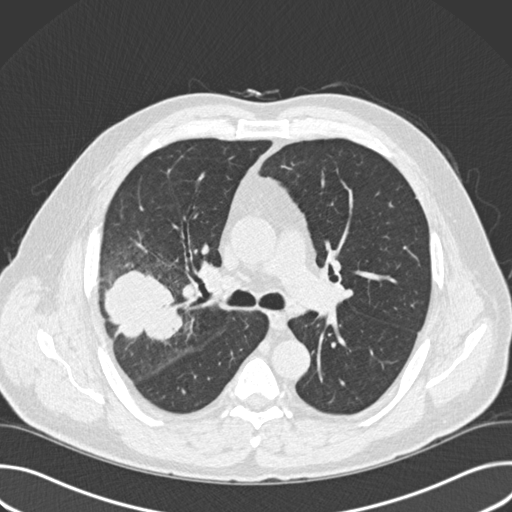
Low-dose screening chest CT, one axial slice. Position 102 of 157 along the scan axis. 120 kVp. Lung window (W 1500 / L -600 HU). 2 mm slice thickness. 512 × 512 image matrix, field of view 380 × 380 mm.
Outlined on this slice (outlined manually by an expert reader):
- lesion 1 (tumor, upper lobe of right lung): bounding box <104,270,183,343> (left, top, right, bottom; pixels)